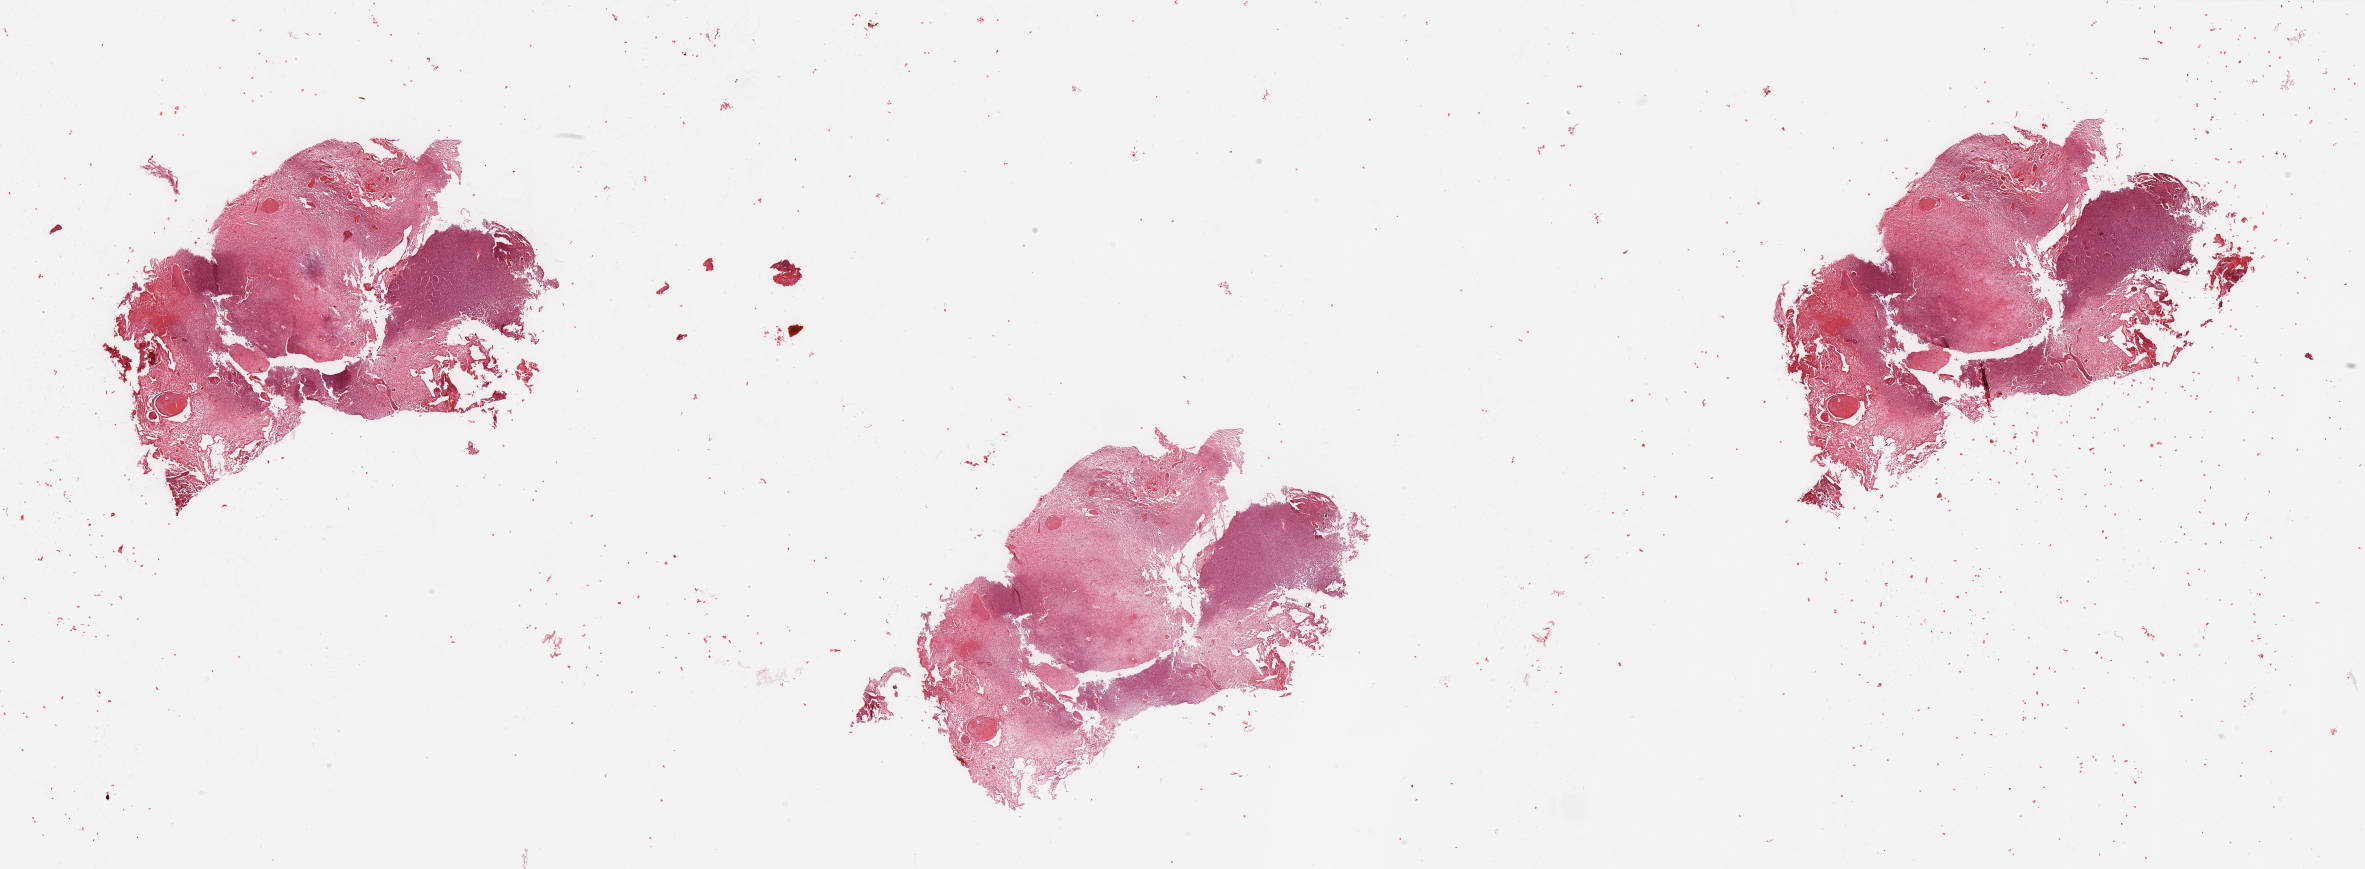
Whole-slide histology image, H&E-stained, a low-resolution overview of the entire scanned area, about 37.4 x 13.7 mm; tumour tissue sample, brain. 65-year-old female patient.
- primary tumour site (as recorded): frontal lobe
- diagnosis: Glioblastoma